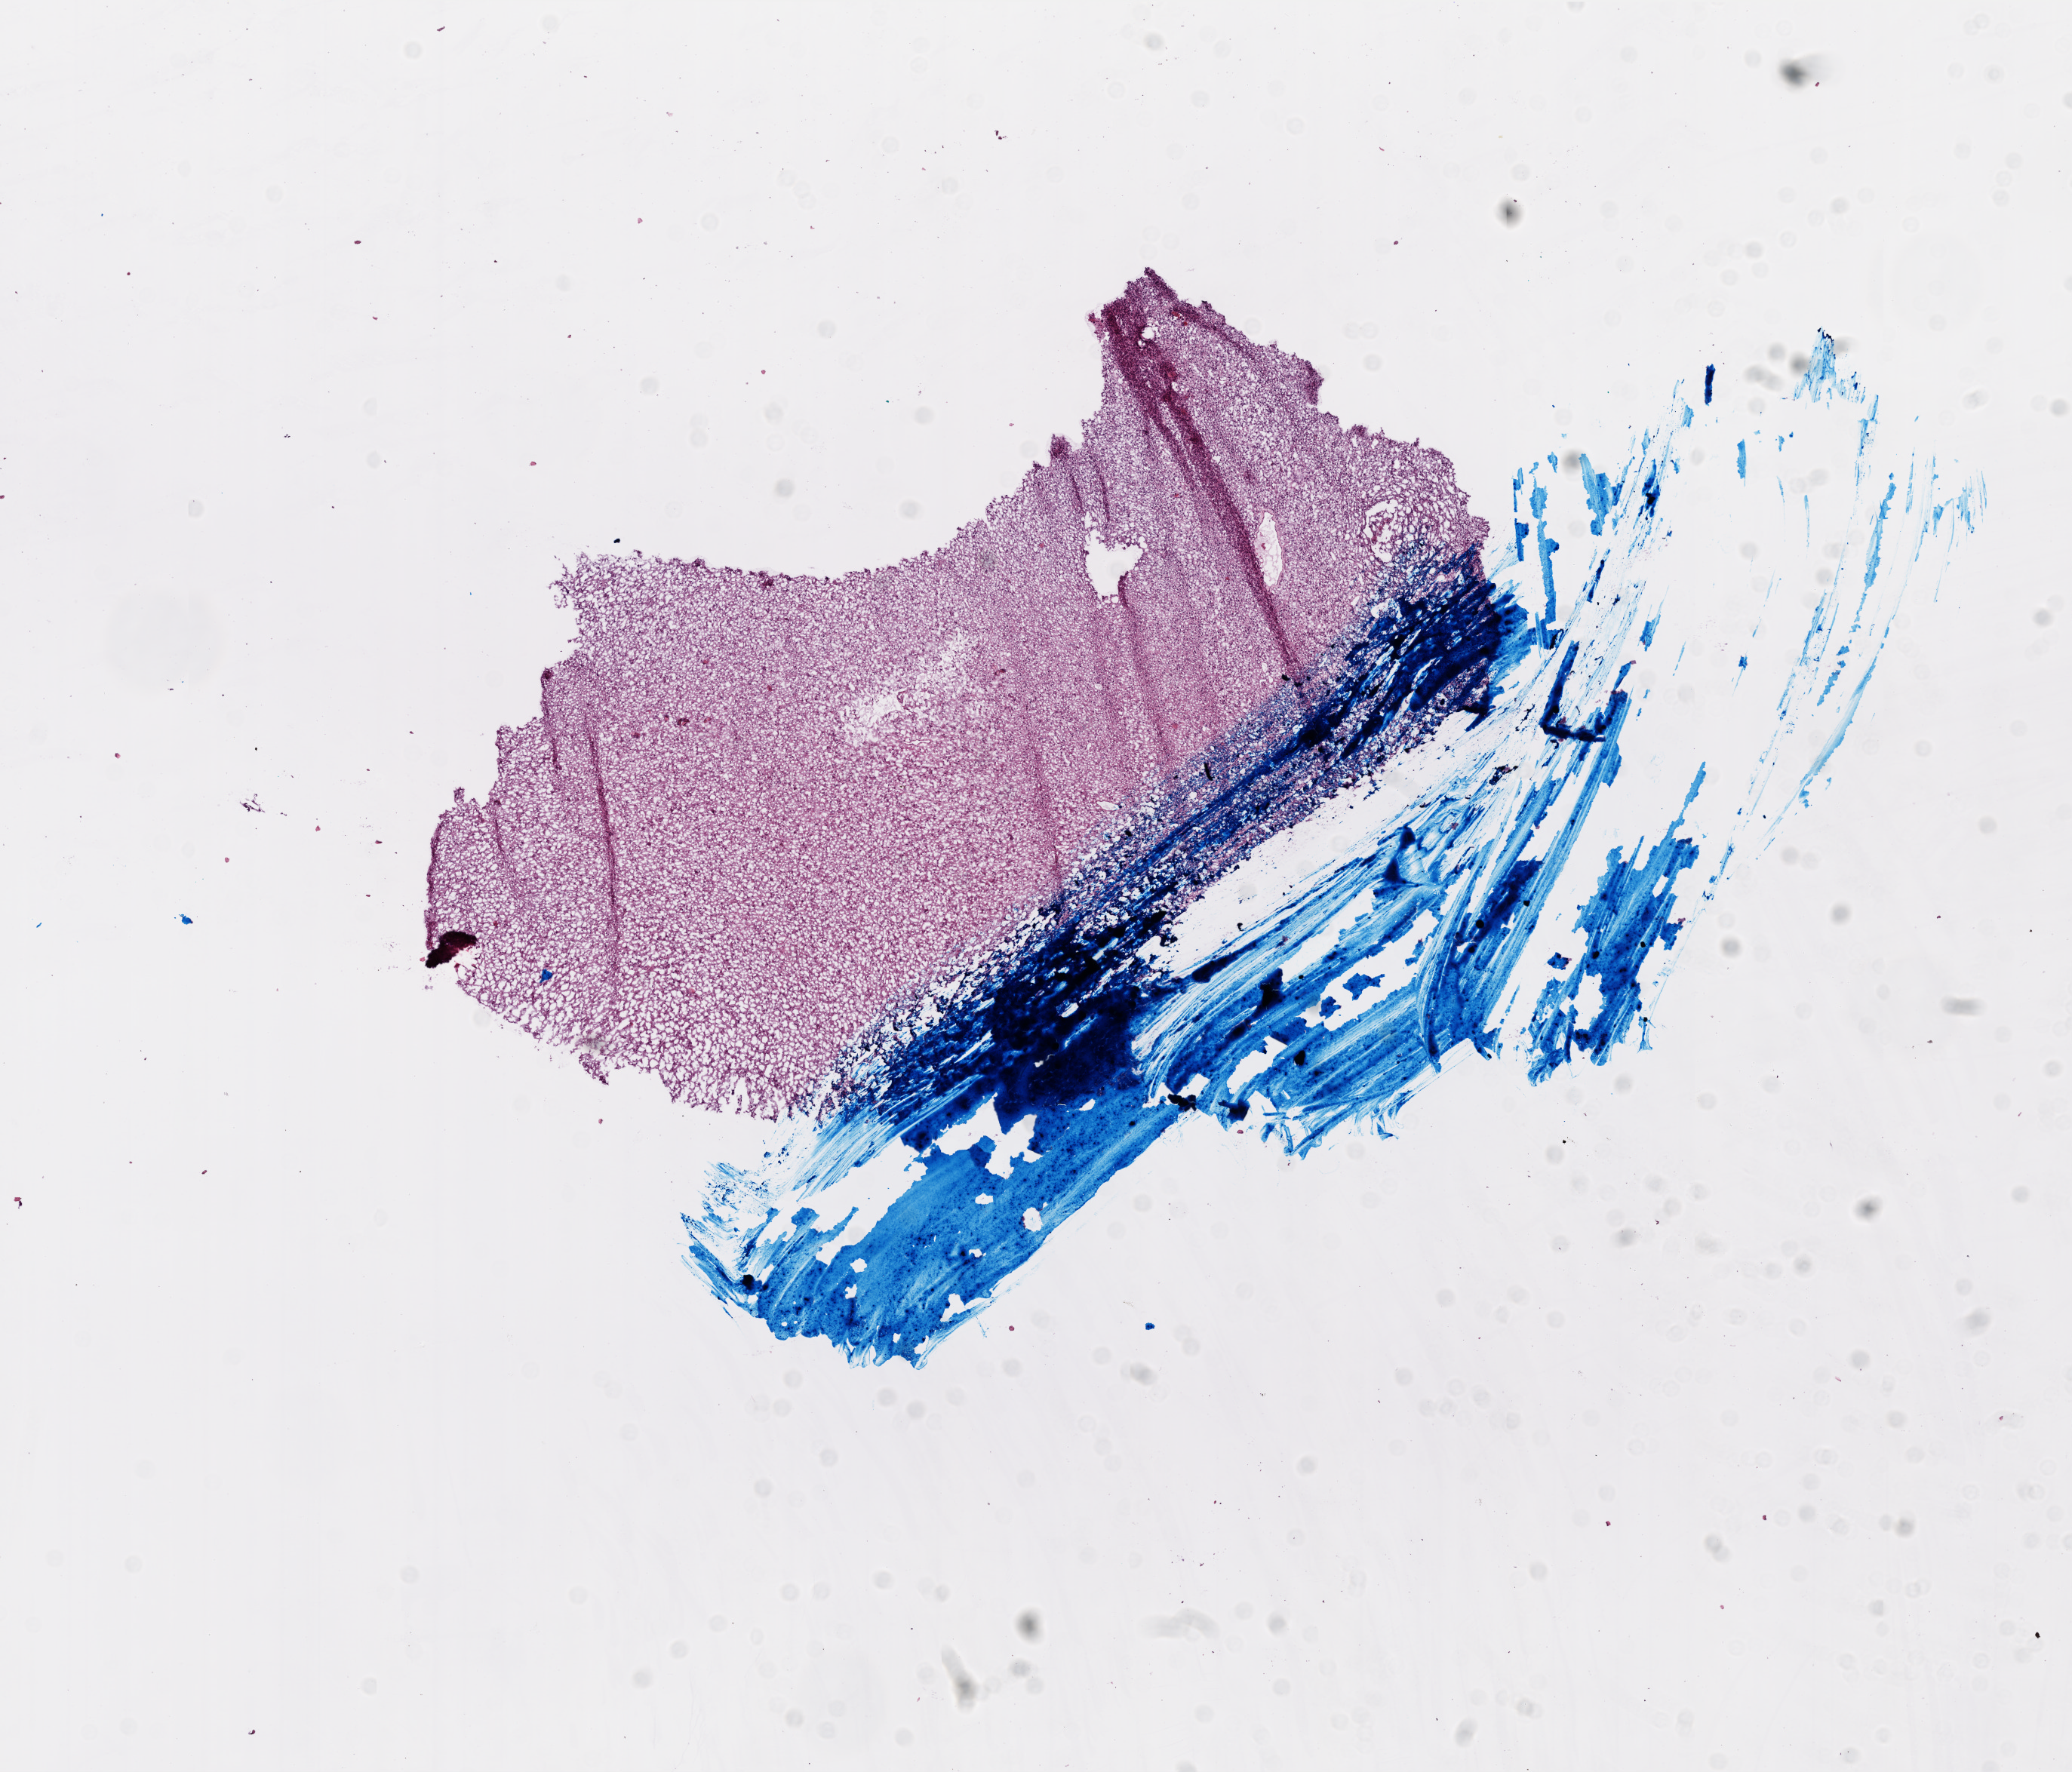
Digitized H&E-stained tissue section (whole slide), shown as a low-resolution overview of the whole scanned area (about 11.0 x 9.4 mm, acquisition: 20x scan); frozen section from the top of the tissue portion; sample: primary tumour, brain. Patient: male, age at initial diagnosis 64 years.
Histologic diagnosis: Glioblastoma.